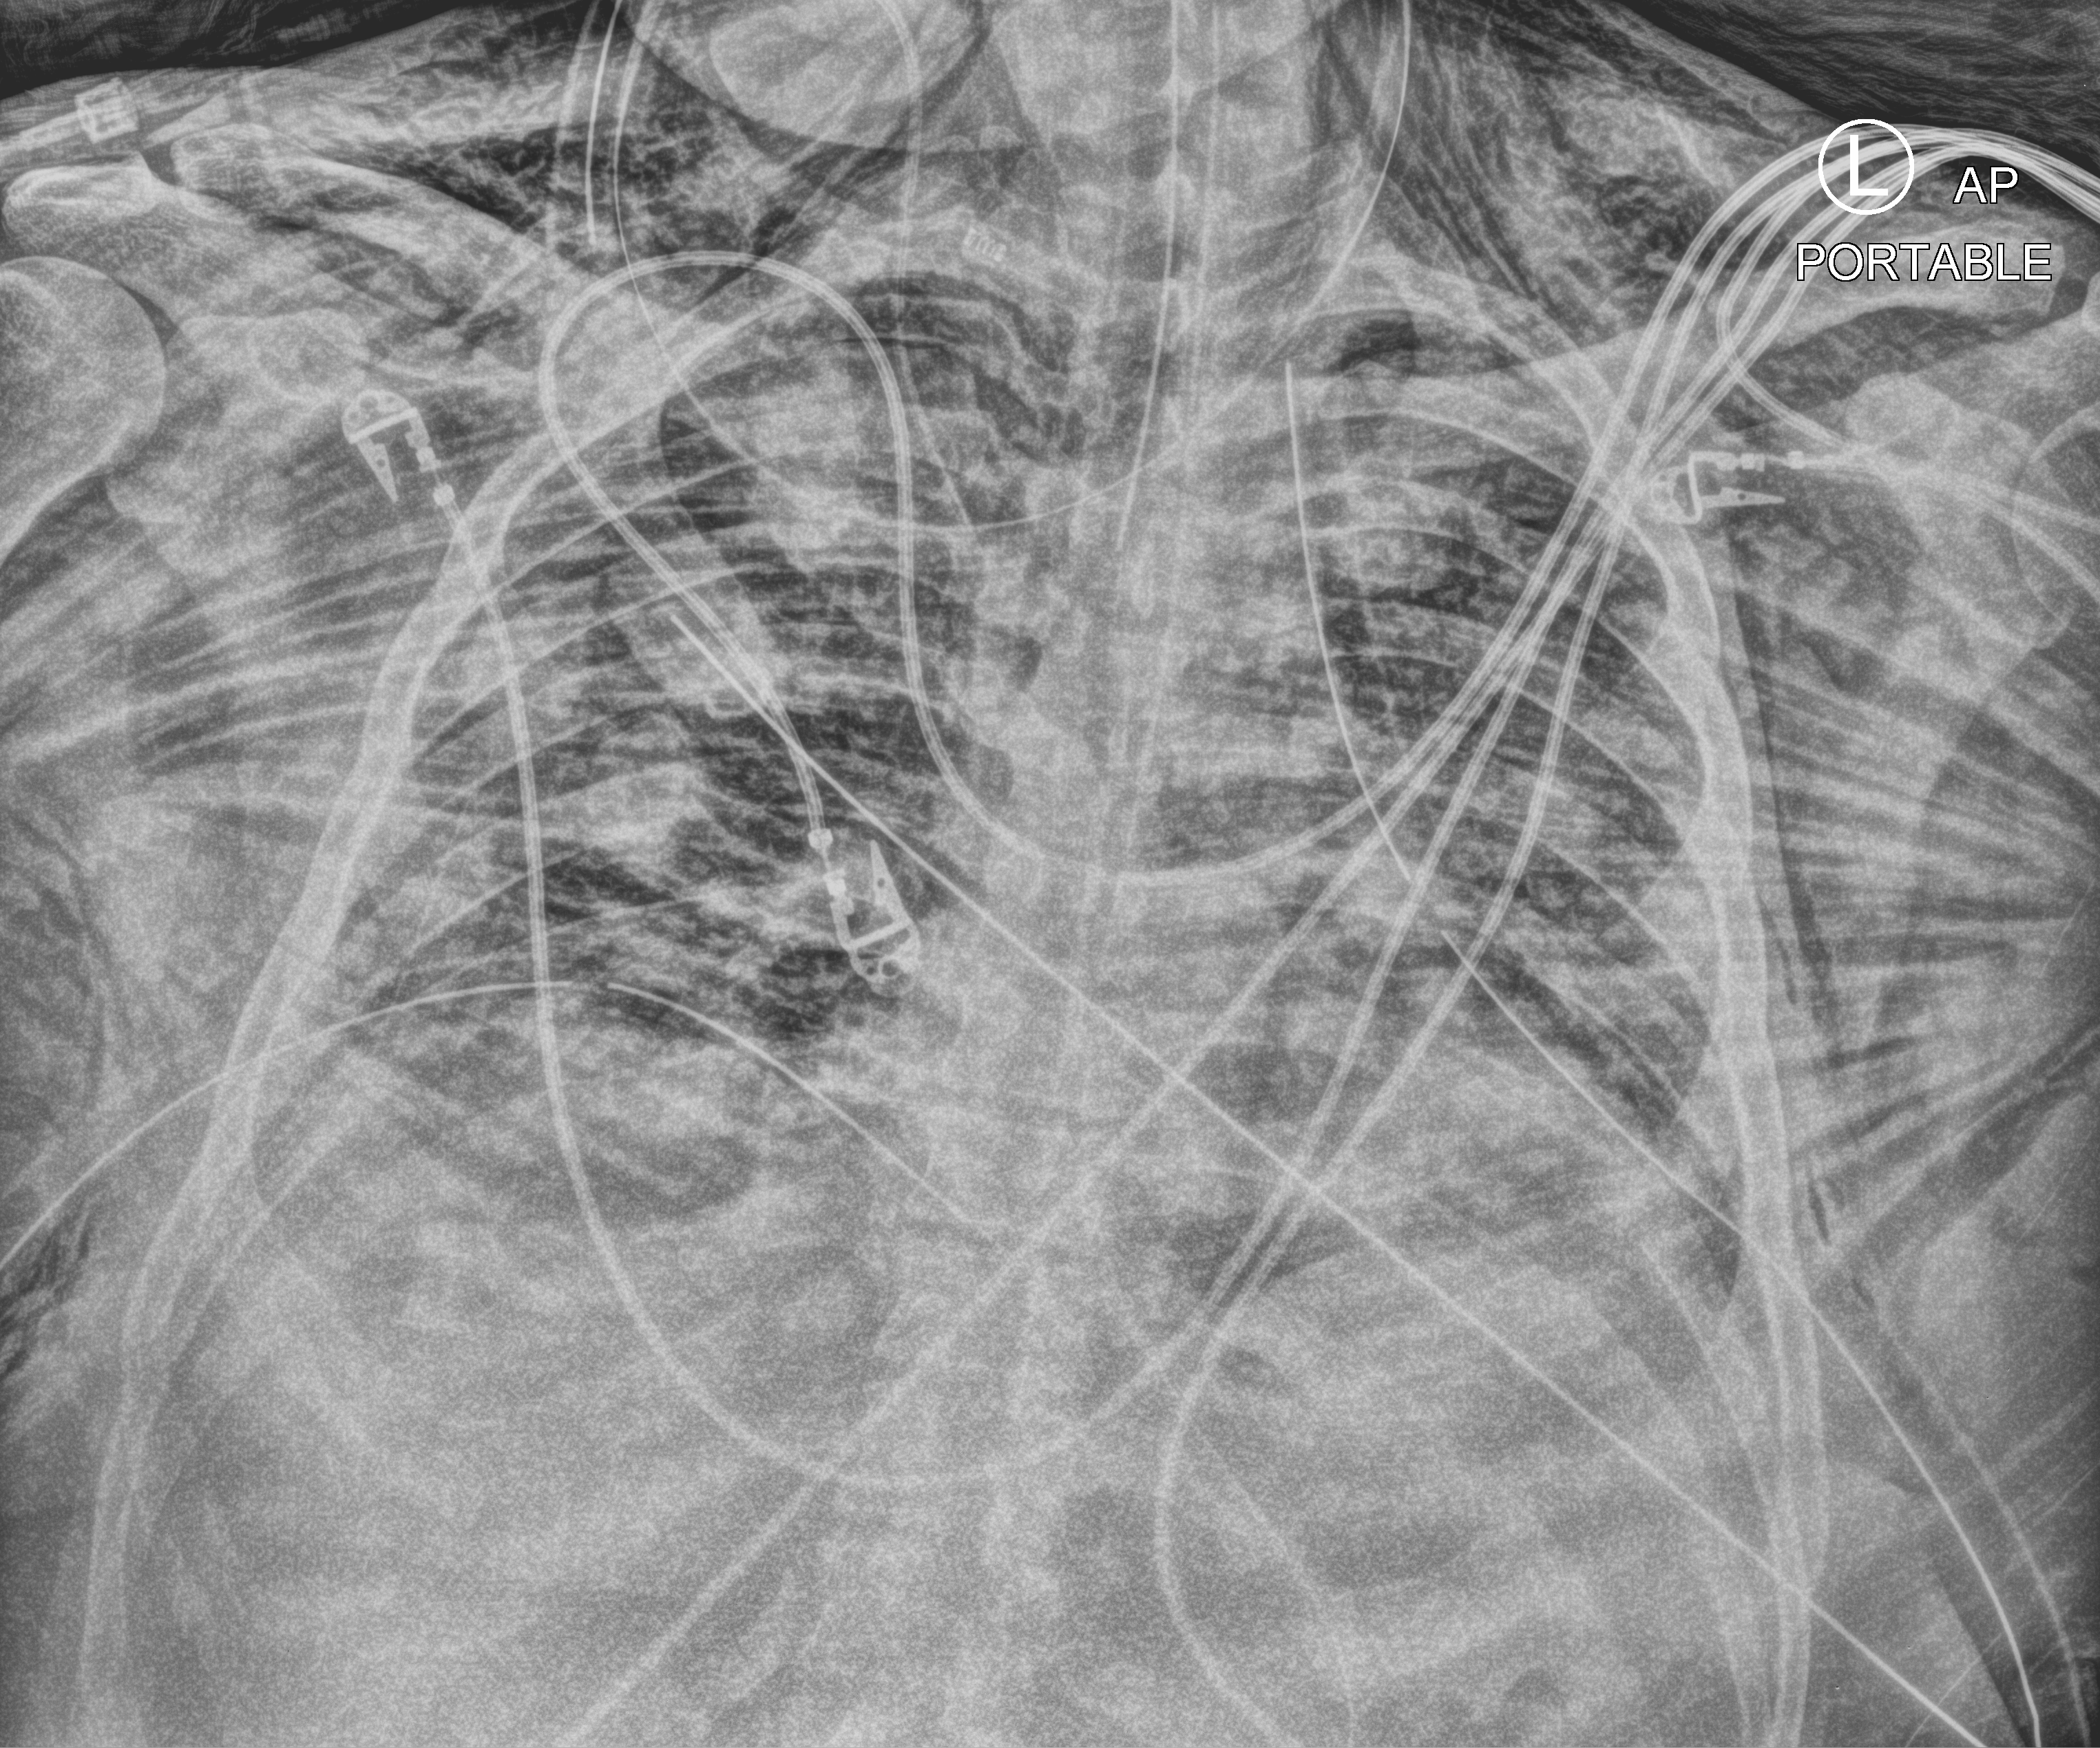
Bedside chest radiograph (computed radiography); anteroposterior (AP) projection. Male patient hospitalised with COVID-19, age 18–59 years.
From the hospital-stay record, not from the radiograph (when in the stay this image was taken is not recorded):
- mechanically ventilated during this hospital stay: yes